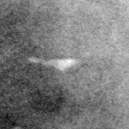
Cropped region of a digitized screen-film mammogram centred on a radiologist-marked abnormality; left breast; CC view; BI-RADS breast density category 3 (scale 1–4).
Calcifications, morphology round and regular / lucent centered; BI-RADS assessment category 2; subtlety rating 3 on a 1 (subtle) to 5 (obvious) scale; benign without callback (not worked up further).